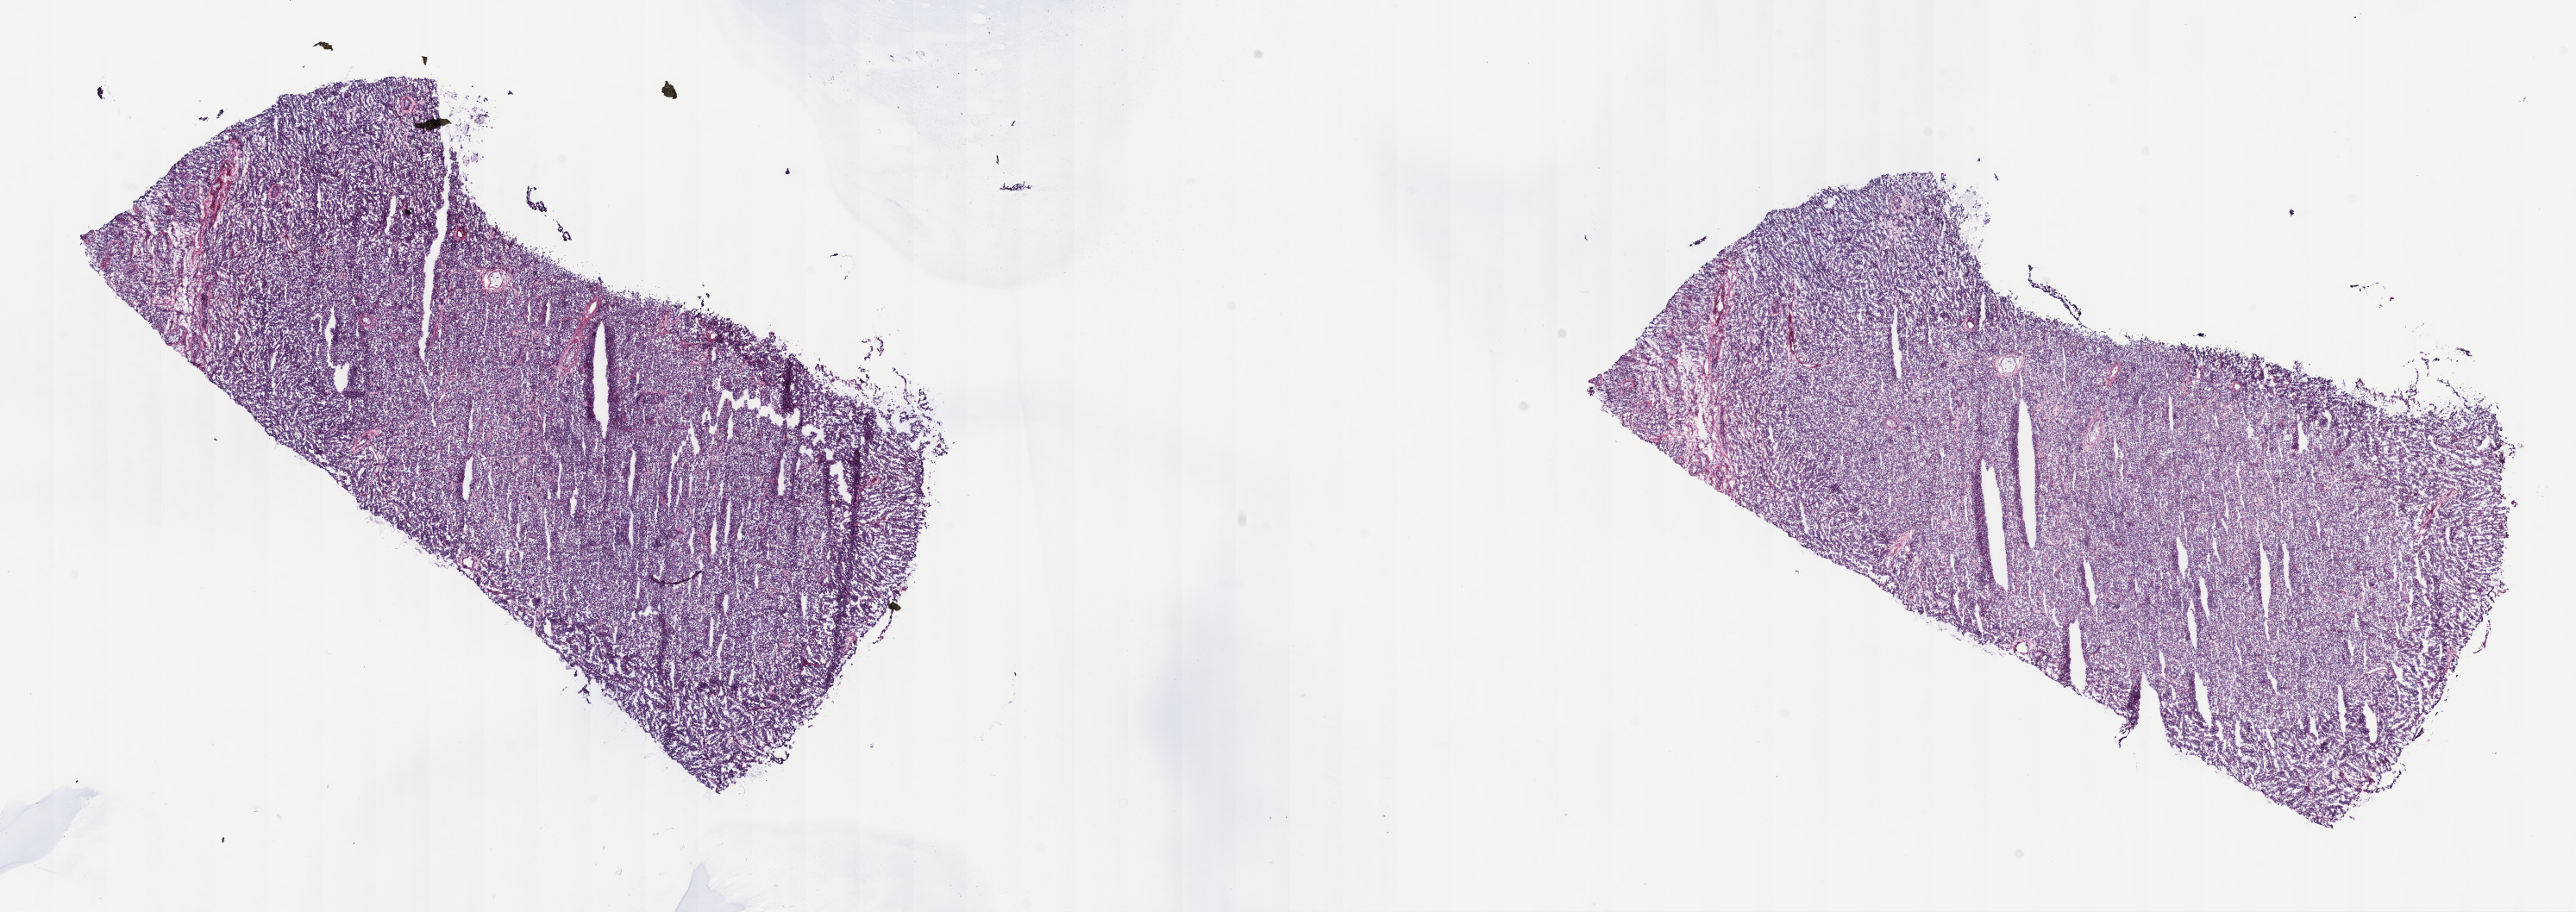
H&E whole-slide image — whole scanned area (about 24.2 x 8.6 mm) shown as a low-resolution overview, frozen section from the top of the tissue portion, sample: additional new primary tumour, testis. Male patient; age at initial diagnosis 28 years. Slide review estimates, as recorded: tumour cells 100%, tumour nuclei 80%, normal cells 0%, stromal cells 0%, necrosis 0%. Infiltration values recorded for this section: lymphocyte infiltration 1%, monocyte infiltration 0%, neutrophil infiltration 0%.
This section: additional new primary tumour. Patient diagnosis: Teratoma, benign.